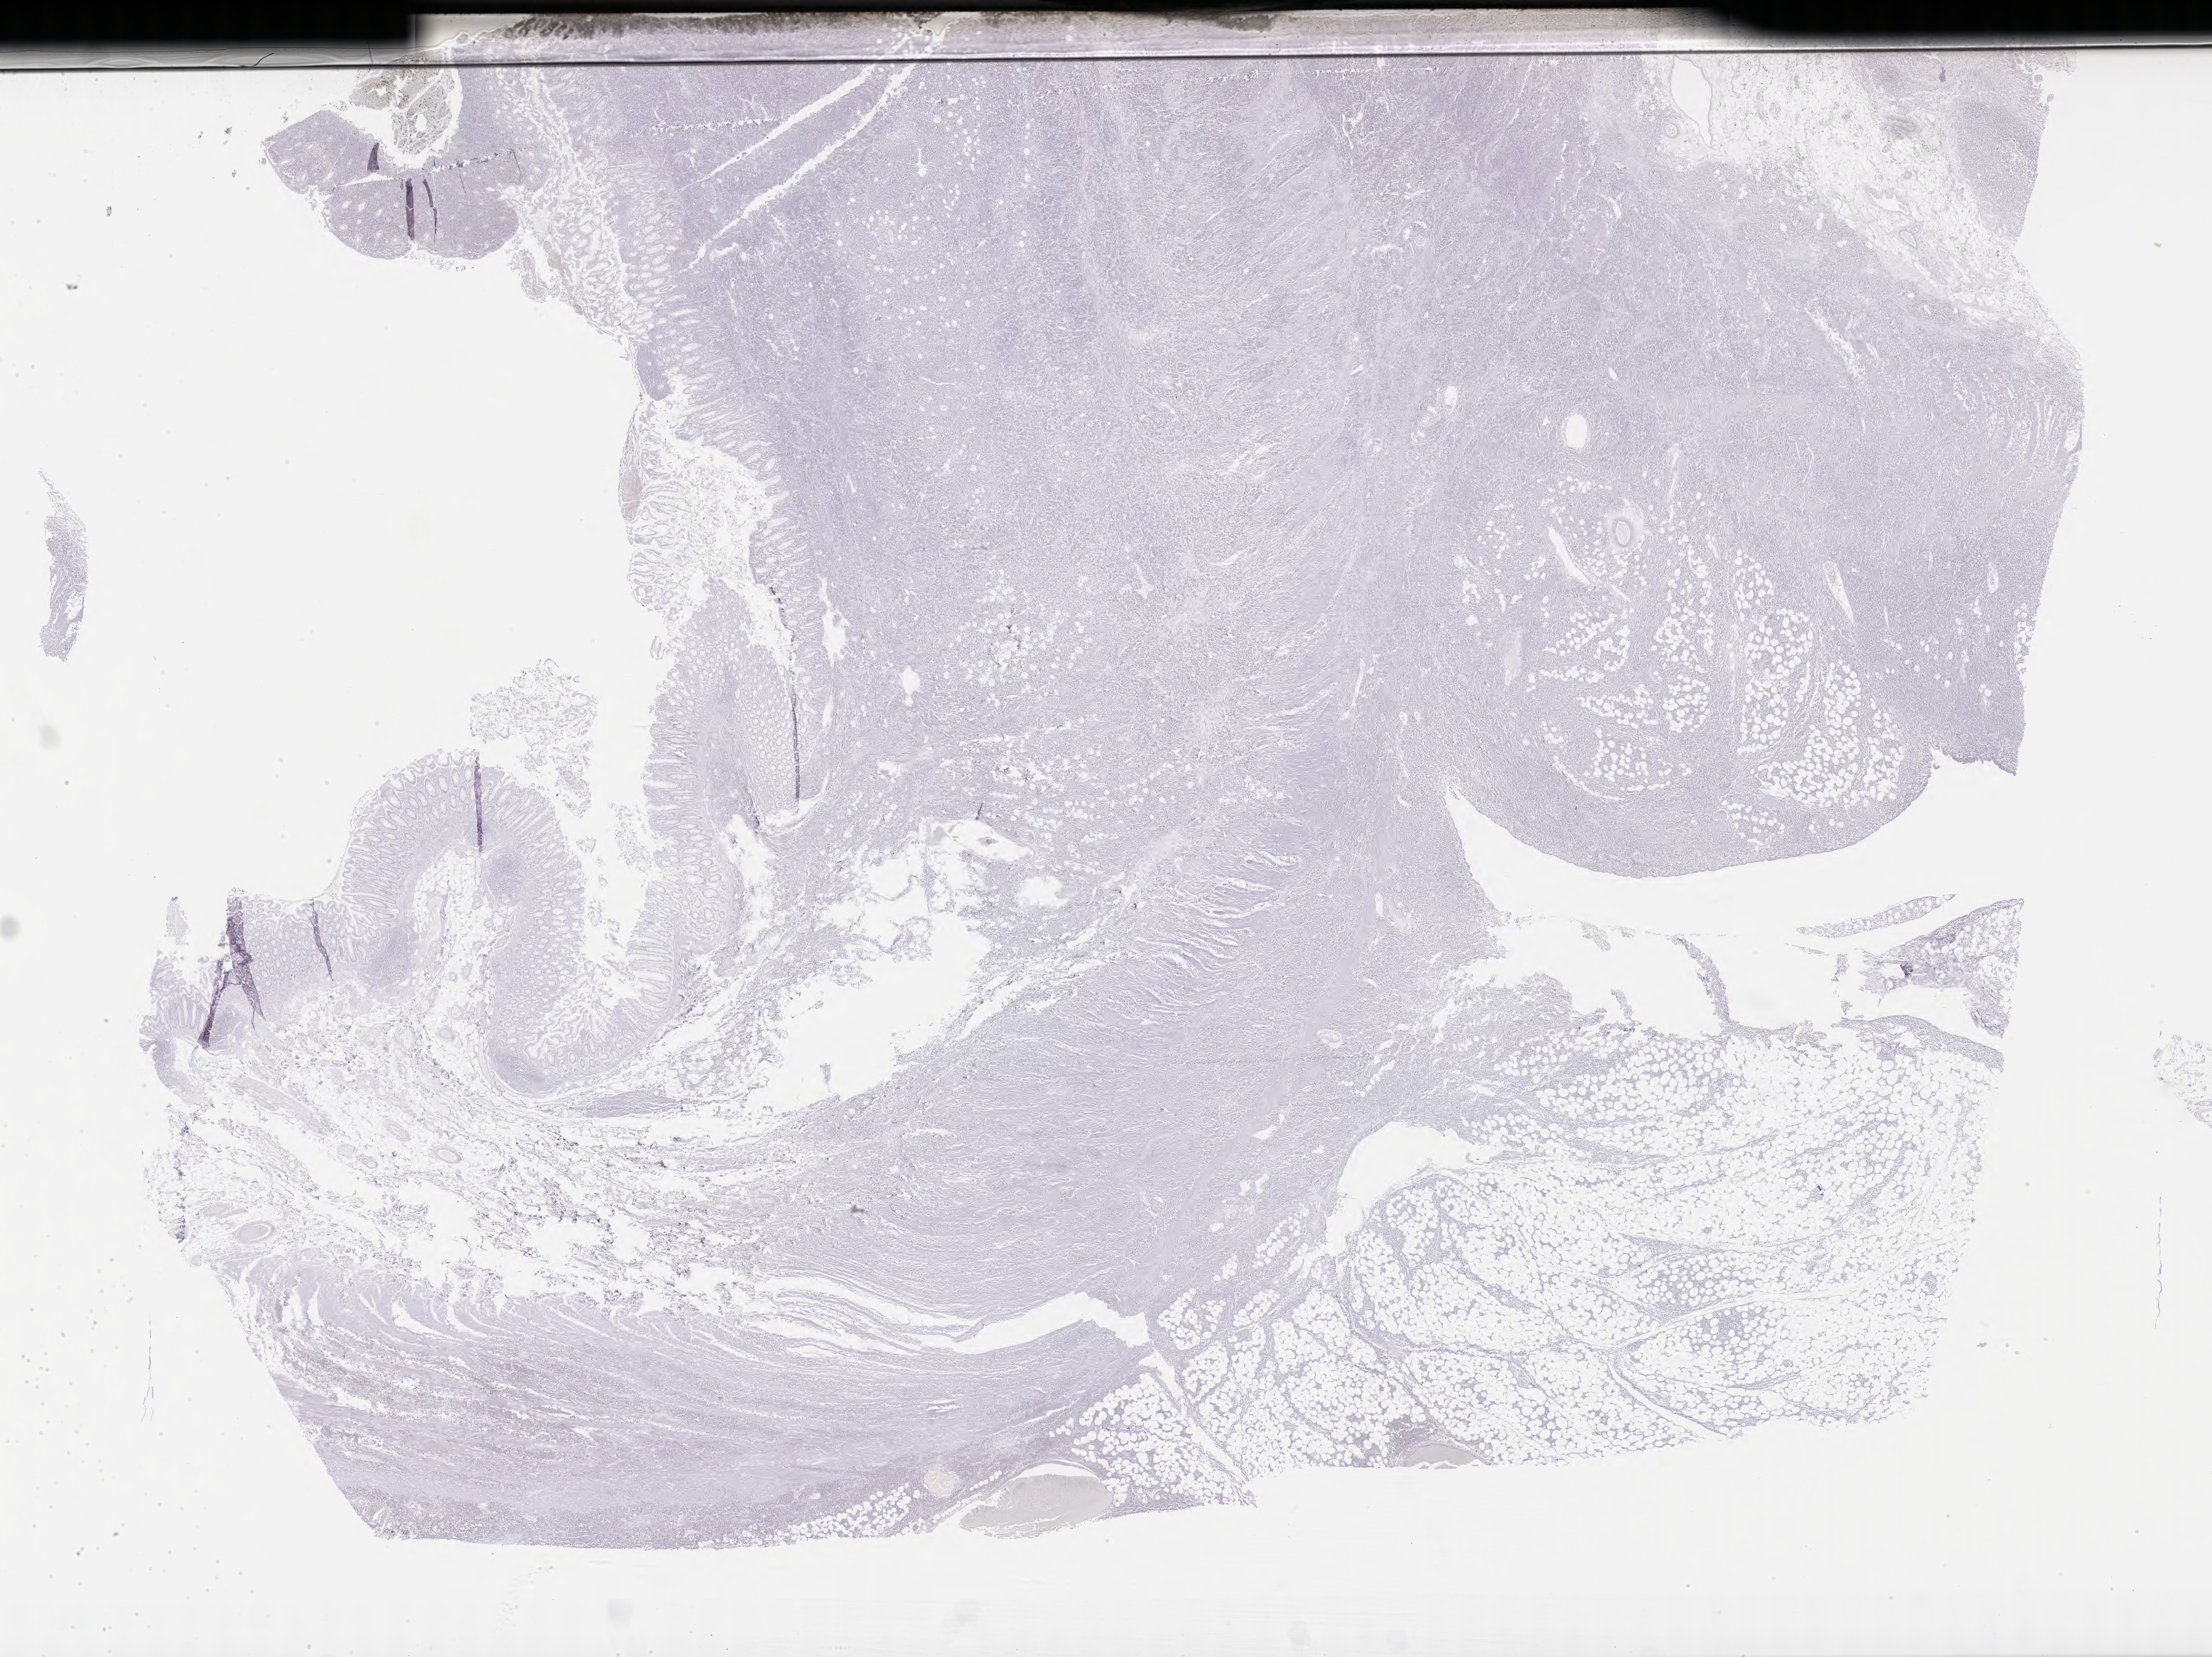
Immunohistochemistry (IHC) whole-slide image stained for BCL6 — low-resolution overview of the scanned area, about 32.2 x 24.1 mm. Tumor tissue. Patient: male, age 56 years.
* diagnosis: Burkitt lymphoma, NOS